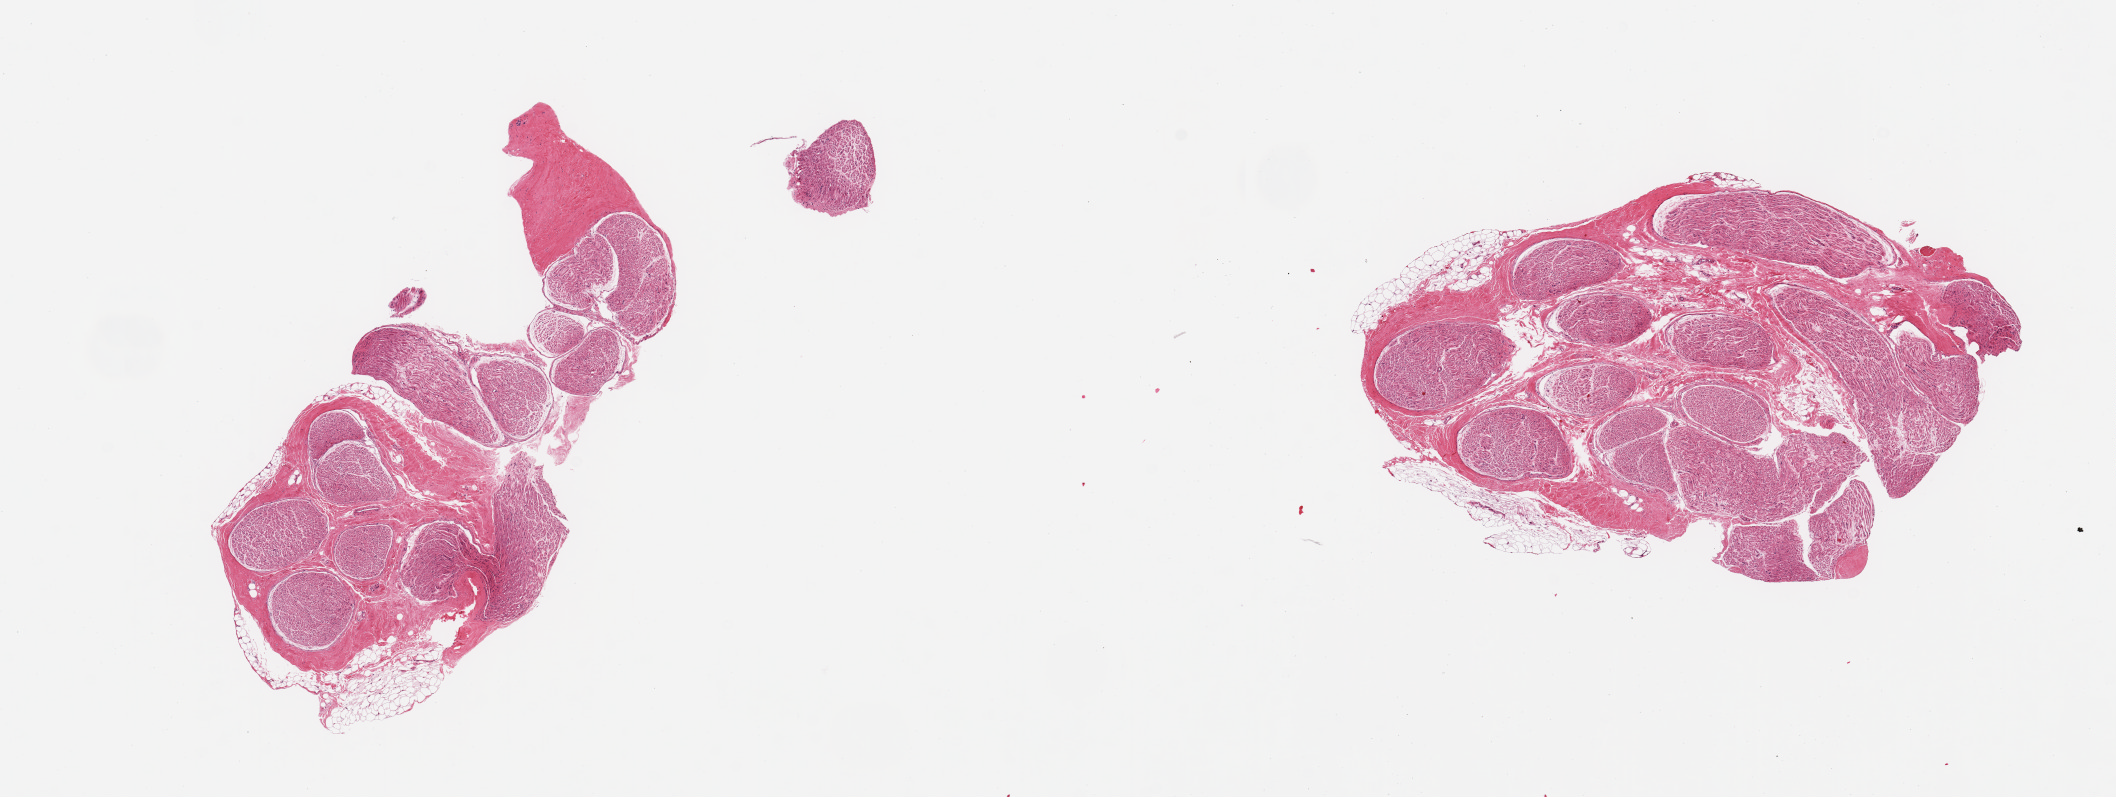
H&E whole-slide image, brightfield — low-resolution overview of the scanned area, about 16.7 x 6.3 mm (slide scanned at 20x), PAXgene-fixed, paraffin-embedded tissue, sampled site (target tissue): tibial nerve, donor tissue sample. Male donor.
Pathologist's review note for this sample: 2 pieces; 1 mmsq external fibrous nodule.